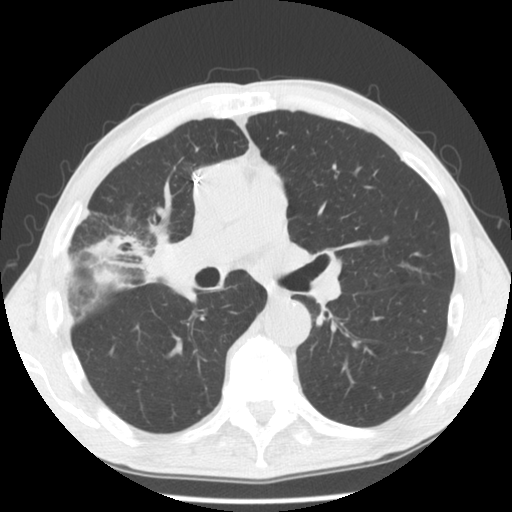
Low-dose screening chest CT, one axial slice. Lung window (W 1500 / L -600 HU). 2.5 mm slice thickness. 512 × 512 image matrix, field of view 334 × 334 mm.
Annotated regions visible in this slice (manually delineated by an expert):
- lesion 1 (tumor, hilum of right lung): bounding box [x1, y1, x2, y2] px = [144, 240, 177, 279]